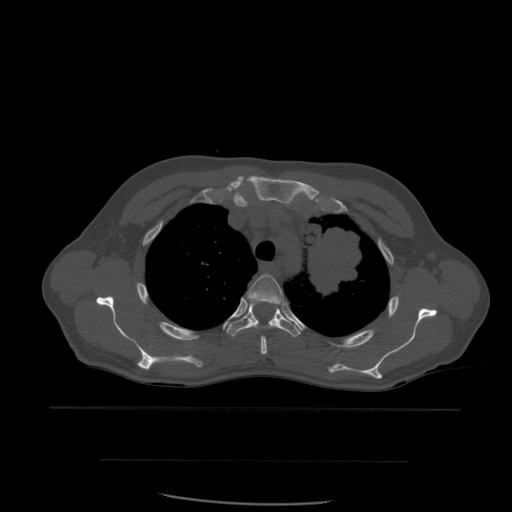
CT including the spine, one axial slice. Bone window (W 1800 / L 400 HU). 512 × 512 image matrix, field of view 392 × 392 mm. Patient age 48 years. Case-level facts recorded for this patient, not image findings: primary cancer: lung; vertebrae with lytic lesions (as recorded): T11.
Structures marked on this image (semi-automatic segmentation, software-assisted and operator-edited):
- T3 vertebra: box from (x=244, y=274) to (x=283, y=355) px
- T4 vertebra: (x=227, y=303)–(x=301, y=337)
- T5 vertebra: (x=275, y=297)–(x=285, y=305)